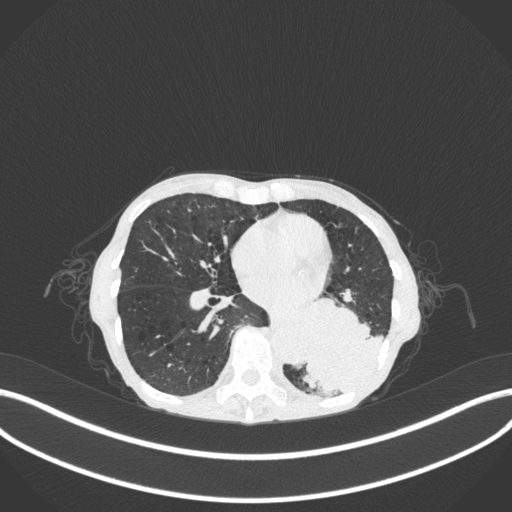
Chest CT, one axial slice. Position 116 of 347 along the scan axis. Reconstruction kernel B31f. 120 kVp. Lung window (W 1500 / L -600 HU). 1 mm slice thickness. 512 × 512 image matrix, field of view 400 × 400 mm. Female patient, age 70 years. Case-level facts recorded for this patient, not image findings: clinical TNM (as recorded): T3 N0 M0; histopathological grade: G3.
Structures marked on this image (rectangle marked by the reading radiologist):
- lung tumour (recorded histology: small cell carcinoma): box from (x=301, y=291) to (x=387, y=396) px